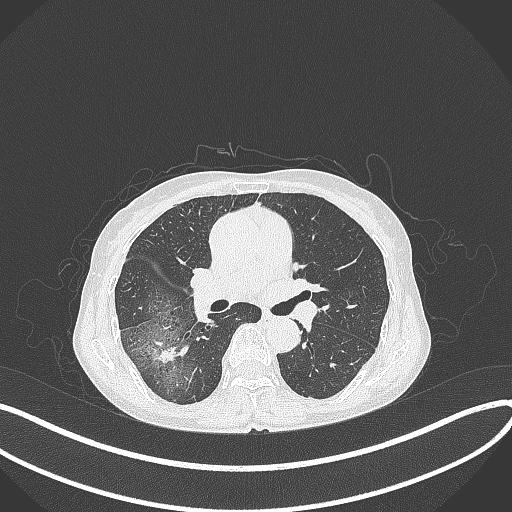
Chest CT, one axial slice; position 226 of 371 along the scan axis; reconstruction kernel B70f; 120 kVp; lung window (W 1500 / L -600 HU); 1 mm slice thickness; 512 × 512 image matrix, field of view 400 × 400 mm. Patient: female, 69 years. From the clinical record (not read from this slice): clinical TNM (as recorded): T1b N0 M0; histopathological grade: G2-3.
Outlined on this slice (rectangle marked by the reading radiologist):
- lung tumour (recorded histology: adenocarcinoma): bounding box <148,336,180,368> (left, top, right, bottom; pixels)